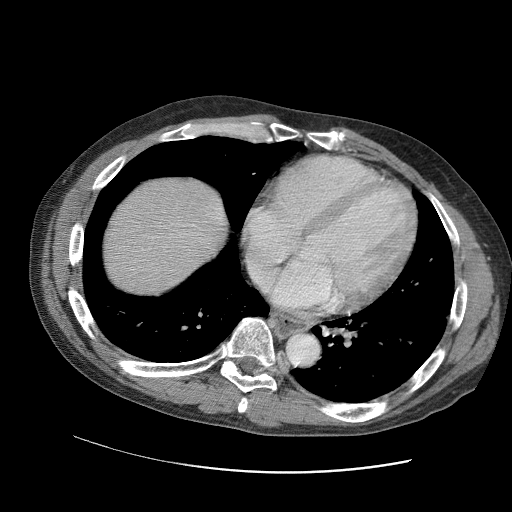
Contrast-enhanced abdominal CT (liver protocol), one axial slice; slice 95 of 109 in the series (ordered by position); reconstruction kernel STANDARD; soft-tissue window (W 400 / L 40 HU); 2.5 mm slice thickness; 512 × 512 image matrix, field of view 400 × 400 mm. Case-level facts recorded for this patient, not image findings: diagnosis: hepatocellular carcinoma (patient treated with transarterial chemoembolisation; whether this scan precedes or follows treatment is not stated here); TNM stage (as recorded): Stage-IIIC; Child-Pugh class: B; tumour nodularity: uninodular.
Structures marked on this image (semi-automatically segmented with operator editing):
- liver parenchyma outside the tumour (the mass and vessels are separate outlines, so this box may not span the whole liver): bounding box [x1, y1, x2, y2] px = [102, 176, 226, 296]
- liver vessels: [162, 213, 180, 249]